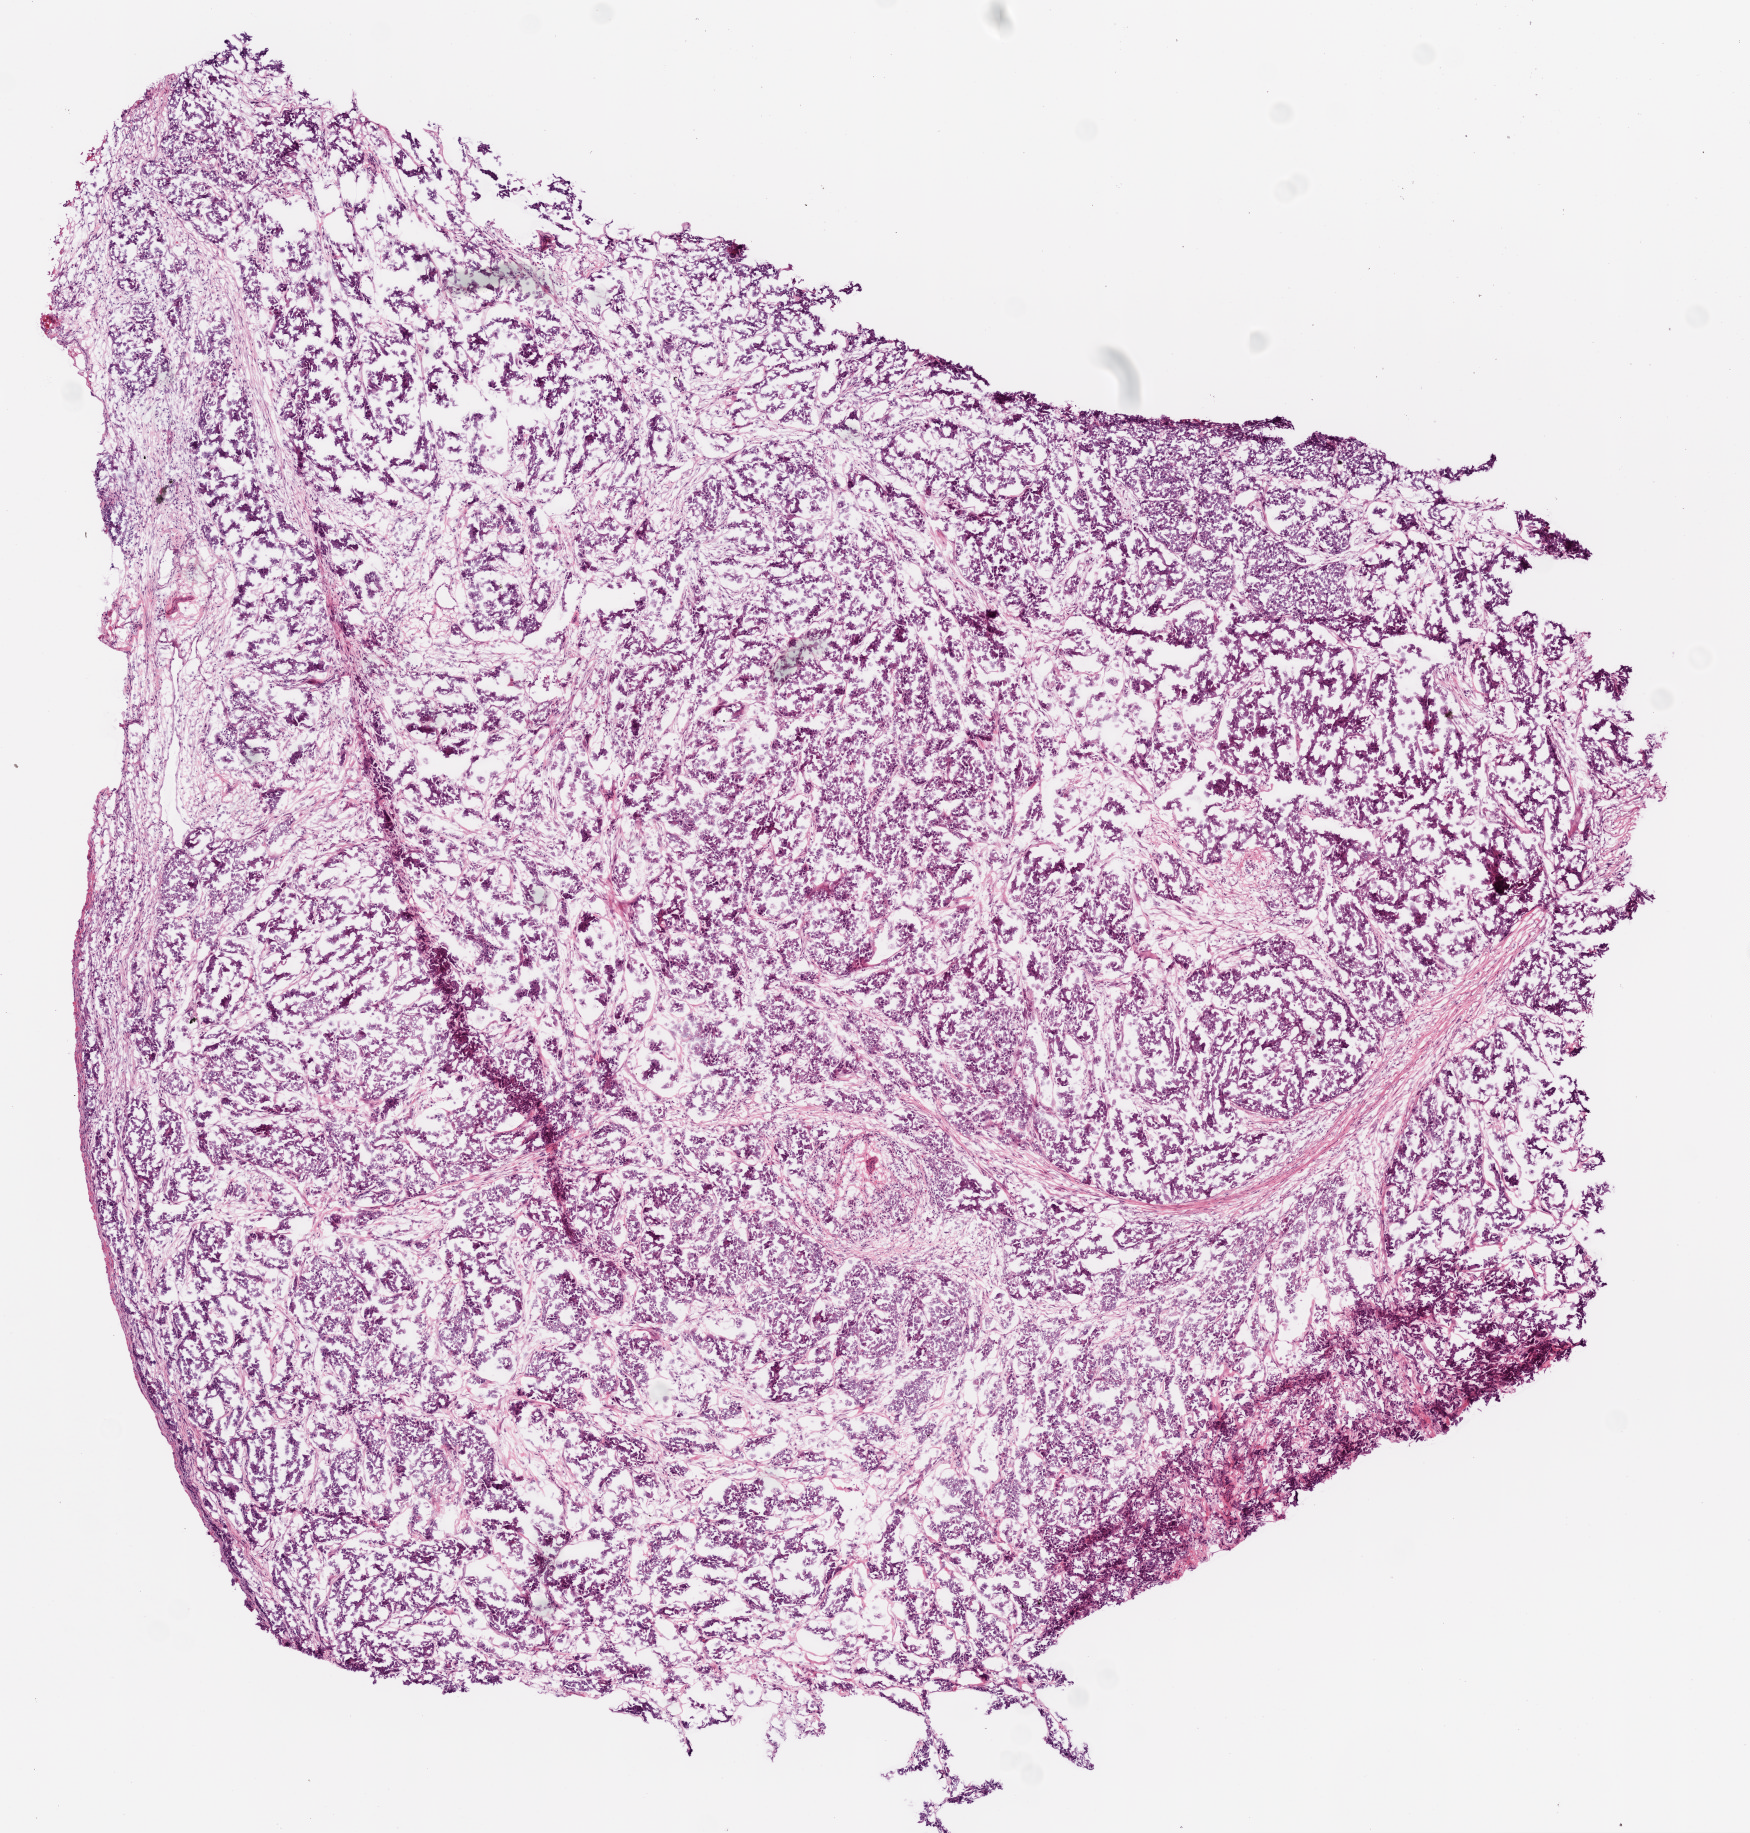
Hematoxylin and eosin (H&E) stained whole-slide image — a low-resolution overview of the entire scanned area, about 7.0 x 7.4 mm, frozen section from the bottom of the tissue portion, sample: primary tumour, ovary. Female patient; age at initial diagnosis 50 years. Histologic grade: G3 (poorly differentiated). Pathologist review of this section (percent, as recorded): tumour cells 90%, tumour nuclei 90%, normal cells 0%, stromal cells 10%, necrosis 0%.
* laterality: left
* FIGO stage: IIIC
* histologic diagnosis: Serous cystadenocarcinoma, NOS